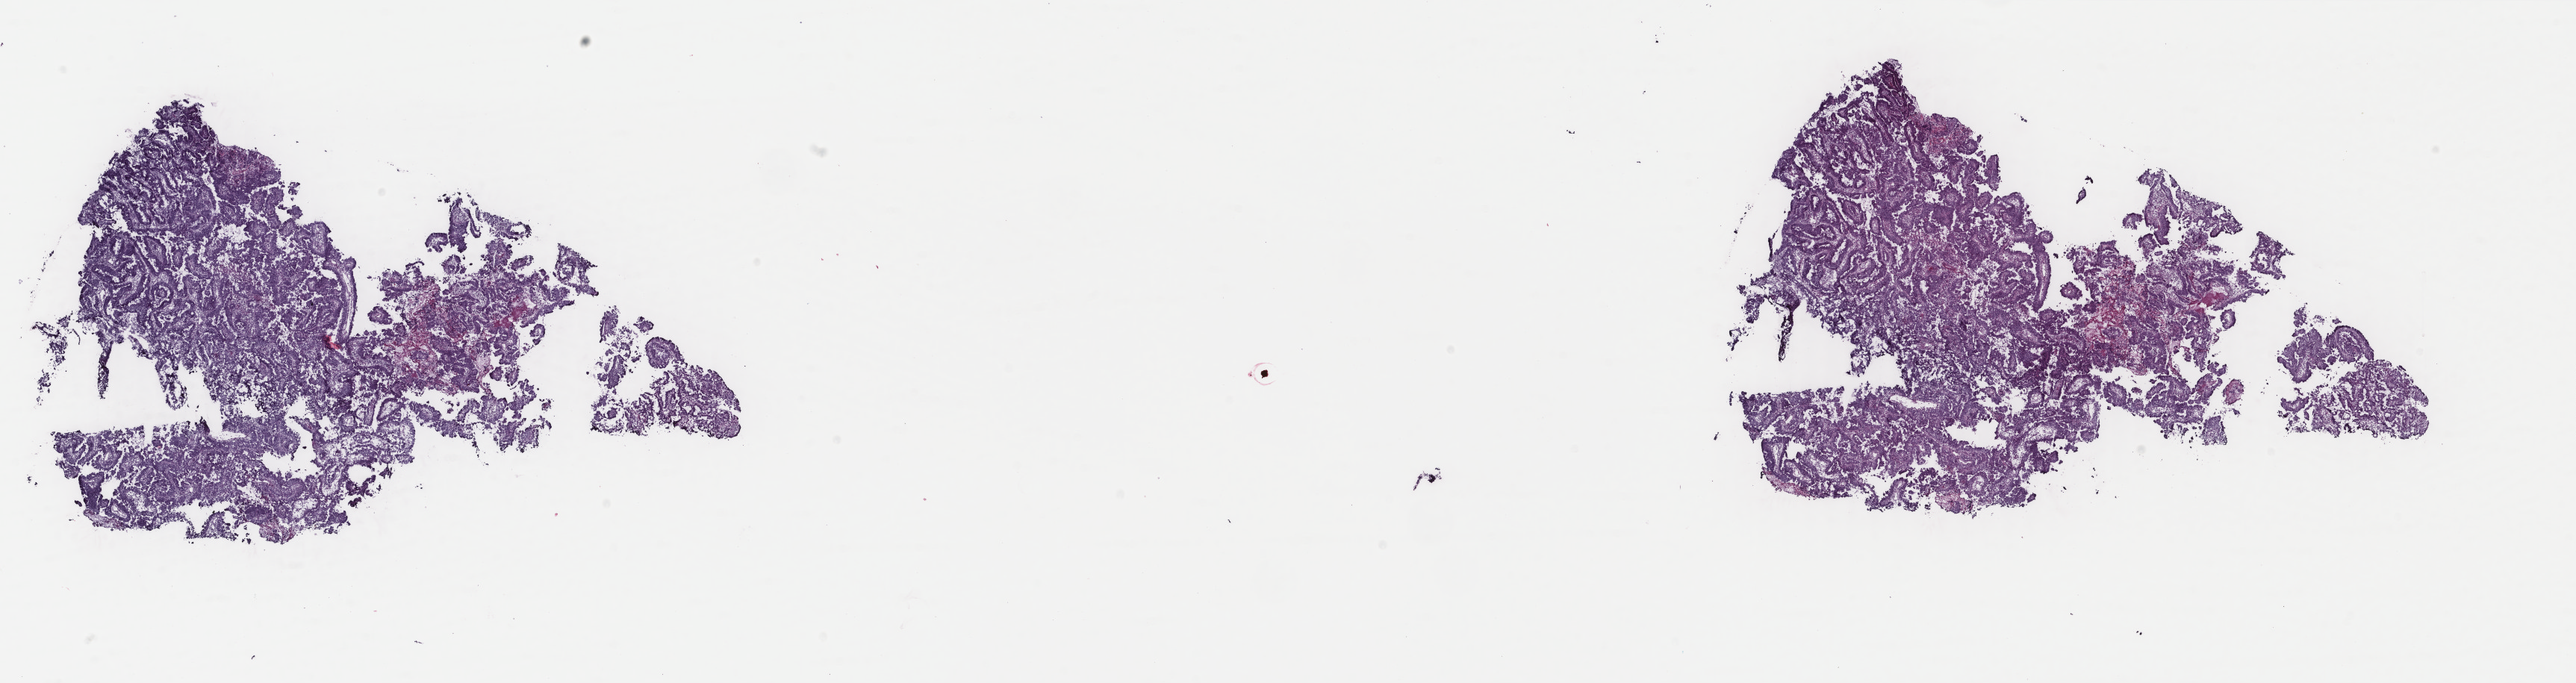
Whole-slide histology image, H&E-stained, low-resolution overview of the scanned area, about 27.4 x 7.3 mm (acquisition: 40x scan), frozen section, sample: primary tumour, uterus. Female patient; age at initial diagnosis 71 years. Histologic grade: G3 (poorly differentiated). Pathologist review of this section (percent, as recorded): tumour cells 95%, tumour nuclei 90%, normal cells 0%, stromal cells 0%, necrosis 5%. Infiltration values recorded for this section: lymphocyte infiltration 1%, monocyte infiltration 1%, neutrophil infiltration 0%.
FIGO stage: IIIC1. Pathologic diagnosis: Serous cystadenocarcinoma, NOS (endometrium).